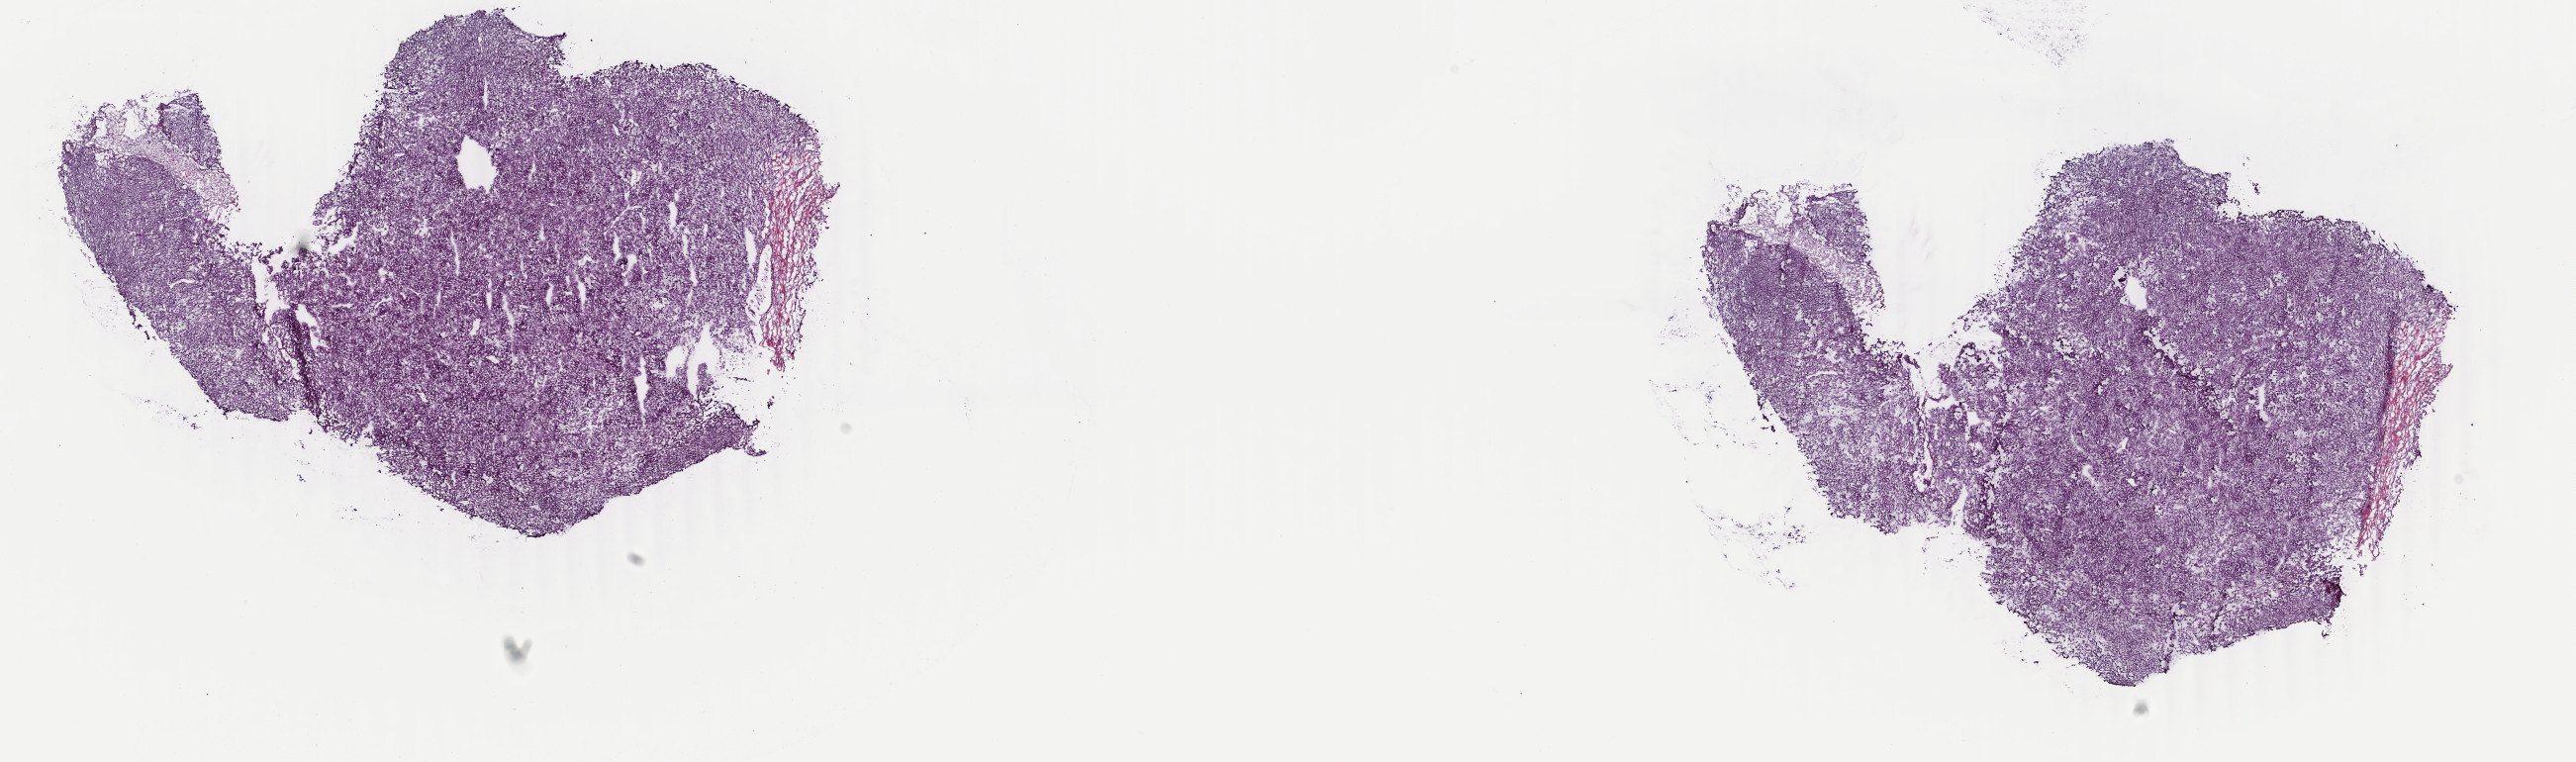
H&E whole-slide image — whole scanned area (about 20.7 x 6.1 mm) shown as a low-resolution overview; frozen section from the top of the tissue portion; sample: primary tumour, adrenal cortex. Female patient; age at initial diagnosis 30 years. Composition of this section per pathologist review: tumour cells 100%, tumour nuclei 80%, normal cells 0%, stromal cells 0%, necrosis 0%. Infiltration values recorded for this section: lymphocyte infiltration 2%, monocyte infiltration 0%, neutrophil infiltration 0%.
Diagnosis: Adrenal cortical carcinoma (cortex of adrenal gland). Lymph nodes positive (case pathology): 0 of 1 examined.